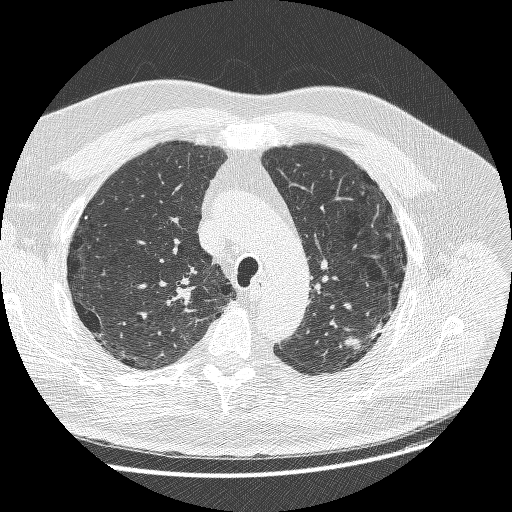
Chest CT (low-dose screening protocol), one axial image, baseline screening round, lung window (W 1500 / L -600 HU), 1.25 mm slice thickness, slice 195 of 258 in the series, 512 × 512 image matrix. Male participant, aged 68 years at enrolment. Former smoker at enrolment.
Lesion marked by an expert reader, box from (x=335, y=308) to (x=390, y=361) px. Reader record for this screening exam (exam-level; its link to the box is not recorded): non-calcified nodule or mass ≥4 mm, left upper lobe, 15 × 14 mm, smooth margins, soft tissue attenuation. Participant outcome: lung cancer diagnosed 19 days after this screen — adenosquamous carcinoma, left upper lobe, poorly differentiated (G3), stage IIIB (AJCC 6th edition), 32 mm at pathology.